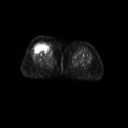
FDG PET of an extremity soft-tissue mass (from a PET/CT study), one axial slice. Position 25 of 267 along the scan axis. 3.27 mm slice thickness. 128 × 128 image matrix, field of view 700 × 700 mm. Female patient, age 56 years. From the clinical record (not read from this slice): histological type: malignant solitary fibrous tumor; grade: intermediate; site of the primary tumour: right thigh.
Annotated regions visible in this slice (expert contour drawn on MRI and transferred to this co-registered scan by the dataset authors):
- gross tumour volume including surrounding oedema: box from (x=36, y=41) to (x=54, y=55) px
- gross tumour volume (mass): (x=37, y=43)–(x=51, y=53)